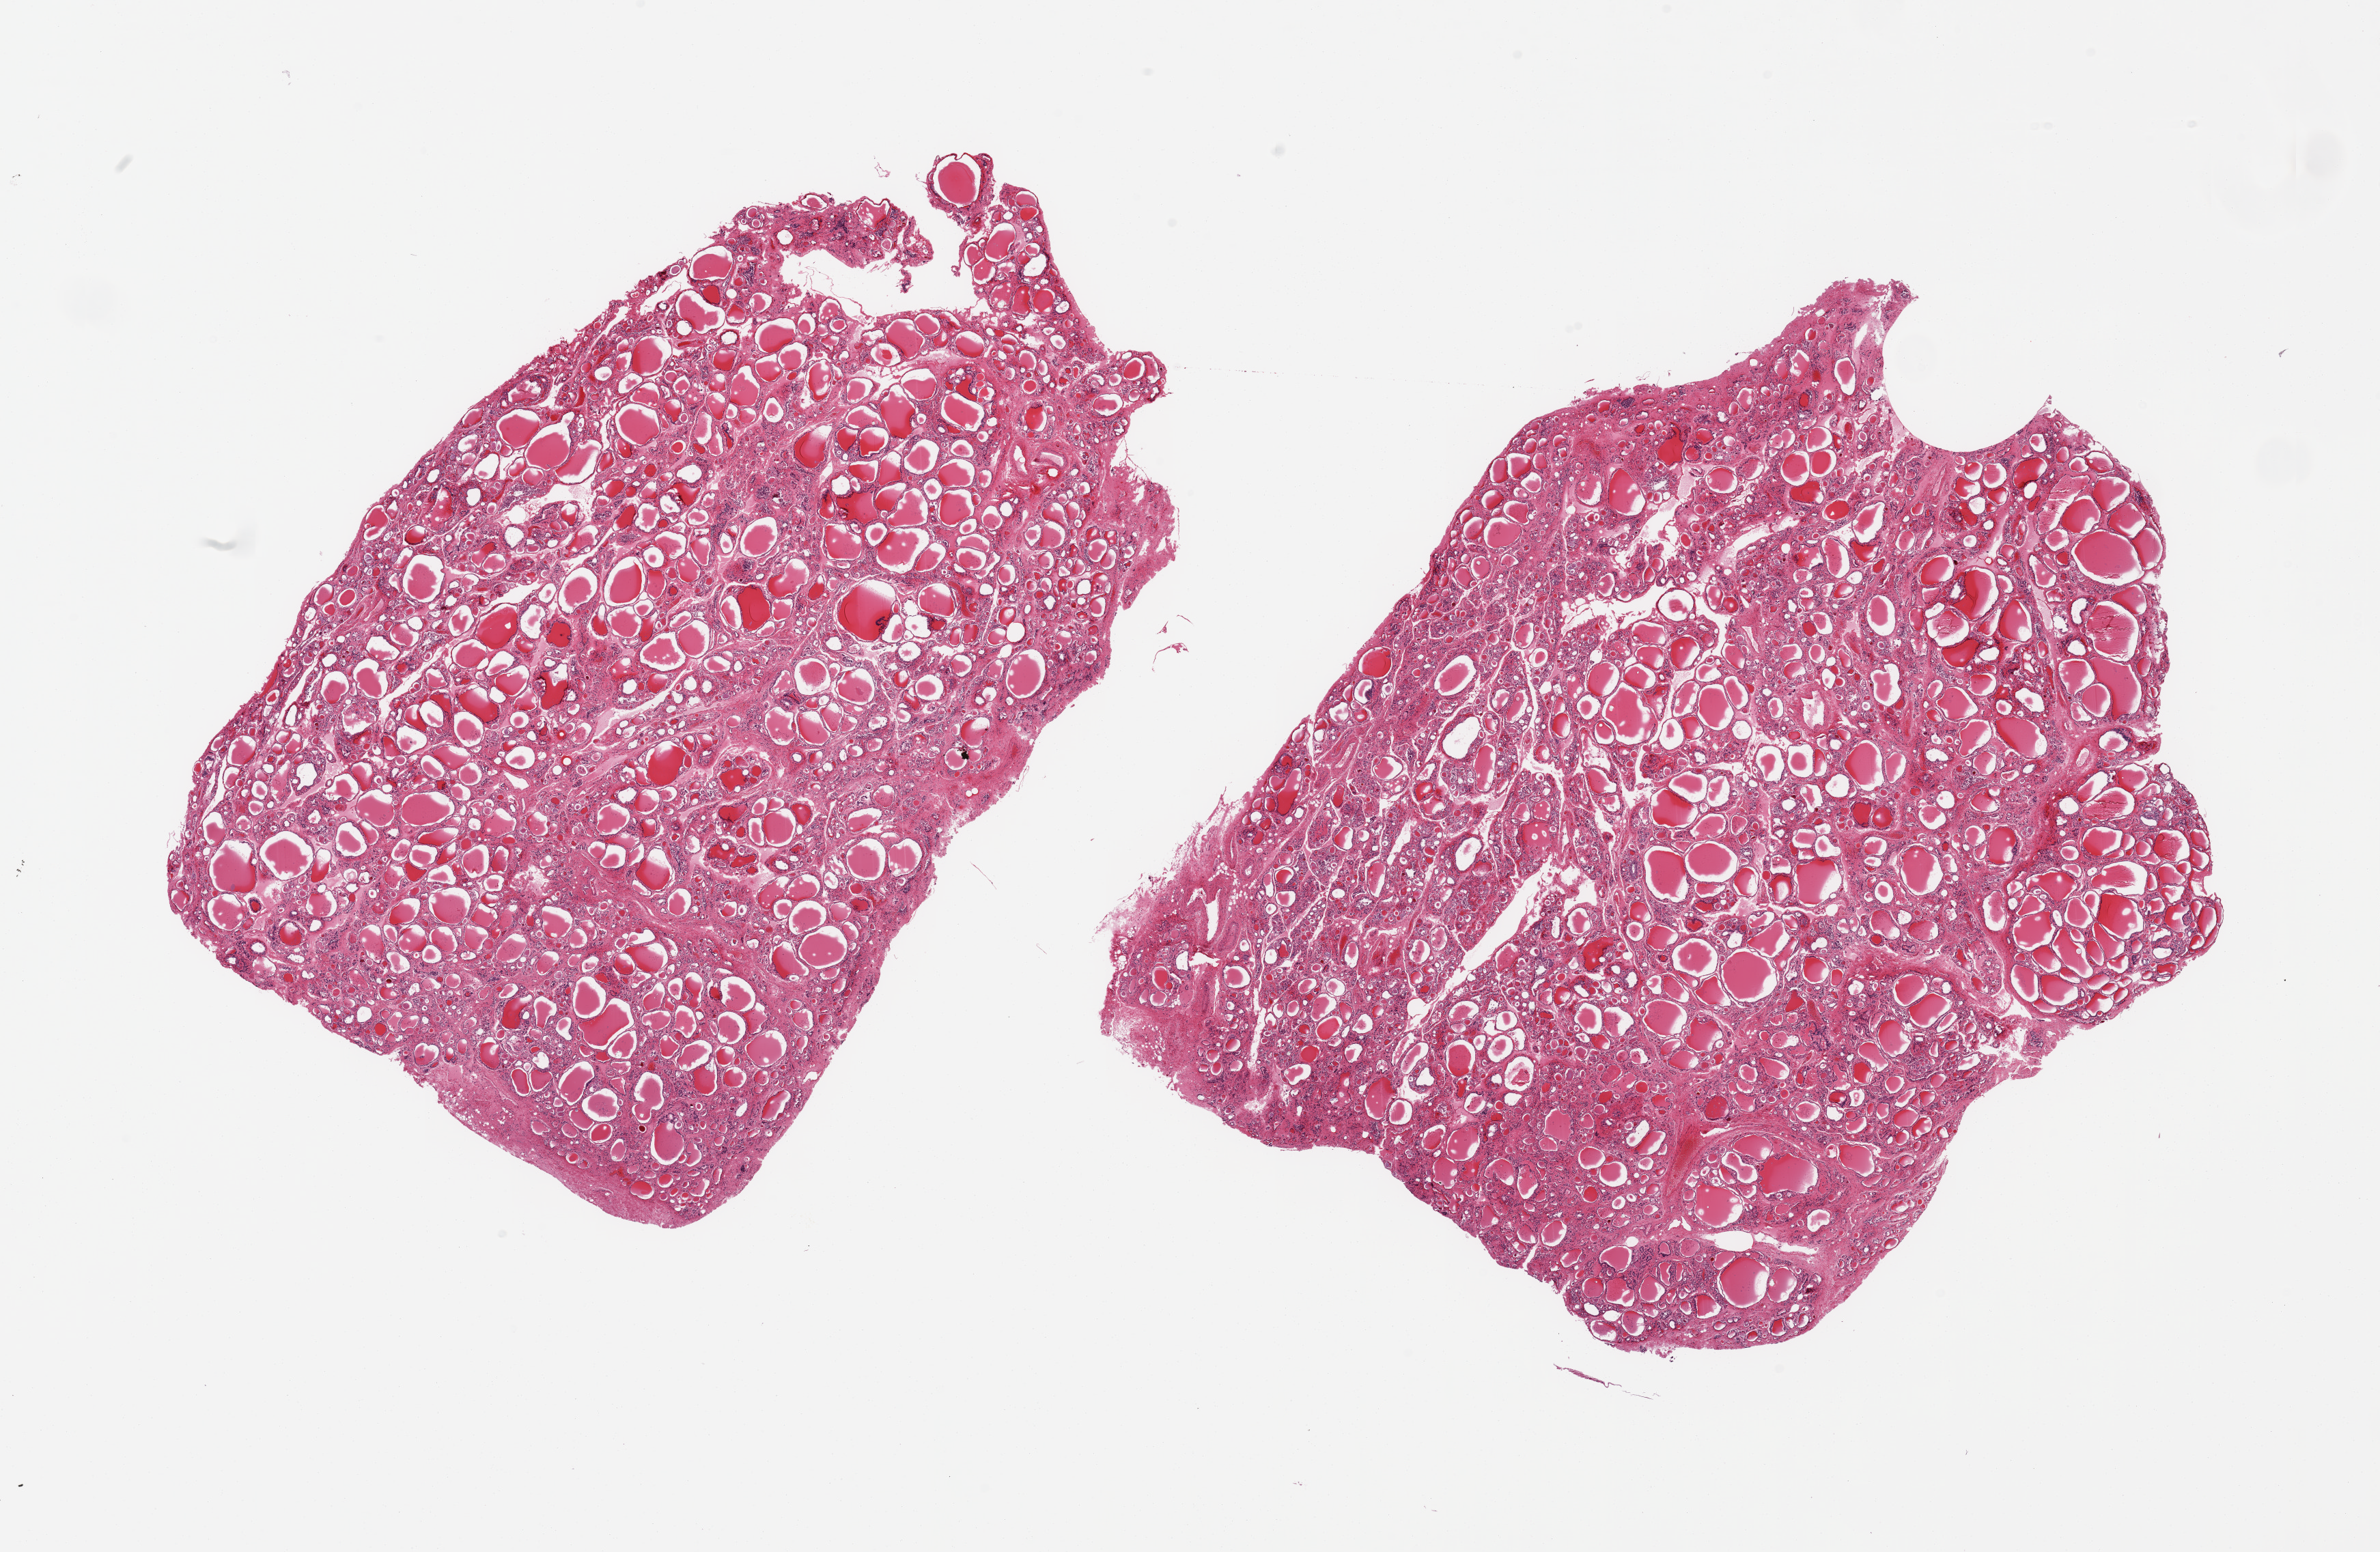
Digitized H&E-stained section — whole scanned area (about 27.6 x 18.0 mm) shown as a low-resolution overview, PAXgene-fixed paraffin-embedded (PFPE) section, section of thyroid (target tissue), tissue donor sample. Donor sex: female.
* reviewer comment on this tissue sample: 2 pieces, no abnormalities